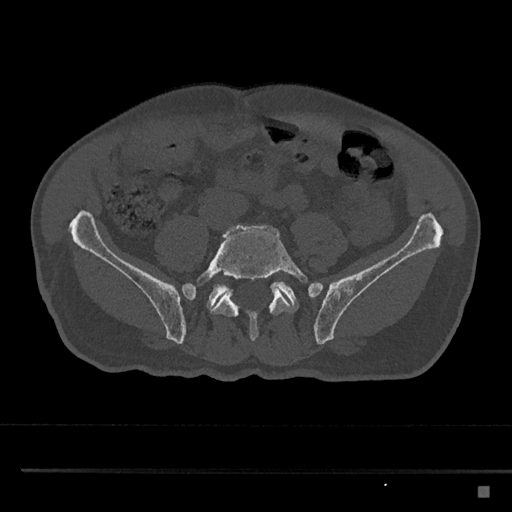
CT including the spine, one axial slice; position 572 of 797 along the scan axis; reconstruction kernel Br40s/3; bone window (W 1800 / L 400 HU); 512 × 512 image matrix. Patient: male, 59 years. Case-level facts recorded for this patient, not image findings: primary cancer: prostate.
Annotated regions visible in this slice (semi-automatically segmented with operator editing):
- L5 vertebra: bounding box [x1, y1, x2, y2] px = [182, 225, 308, 341]